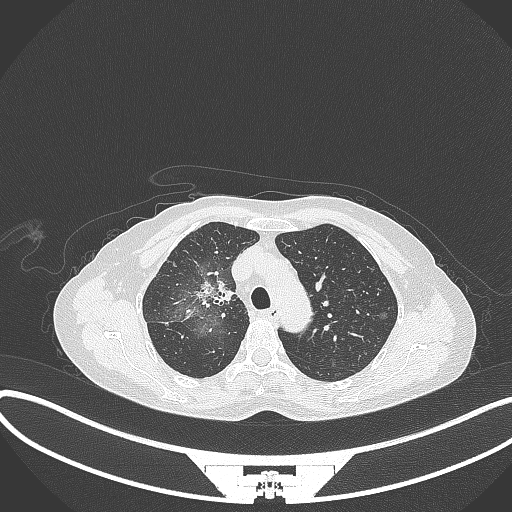
Chest CT, one axial slice. Slice 230 of 284 in the series (ordered by position). Reconstruction kernel B70f. 120 kVp. Lung window (W 1500 / L -600 HU). 1 mm slice thickness. 512 × 512 image matrix. Female patient, age 59 years. From the clinical record (not read from this slice): clinical TNM (as recorded): T3 N0 M0.
Structures marked on this image (bounding box drawn by a radiologist):
- lung tumour (recorded histology: adenocarcinoma): bounding box <194,277,236,311> (left, top, right, bottom; pixels)